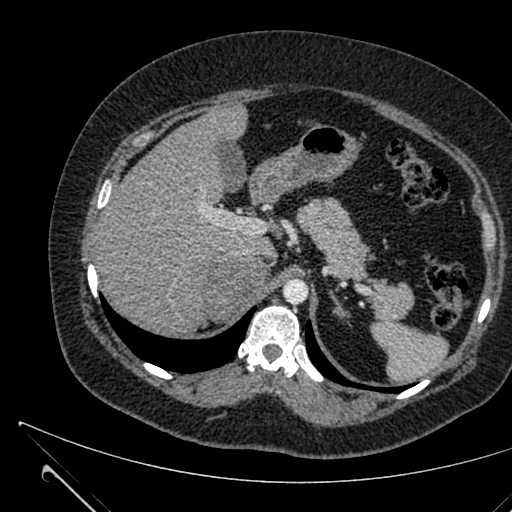
Contrast-enhanced abdominal CT, one axial slice. 120 kVp. Intravenous contrast given. Soft-tissue window (W 400 / L 40 HU). 1 mm slice thickness. 512 × 512 image matrix, field of view 376 × 376 mm. Patient: female, 36 years. Case-level facts recorded for this patient, not image findings: diagnosis: adrenocortical carcinoma; tumour side: right adrenal; tumour size at pathology: 10 cm; Ki-67 index: 20 %; stage (as recorded): 4.
Annotated regions visible in this slice (semi-automatically segmented with operator editing):
- mass: bounding box <204,257,264,321> (left, top, right, bottom; pixels)